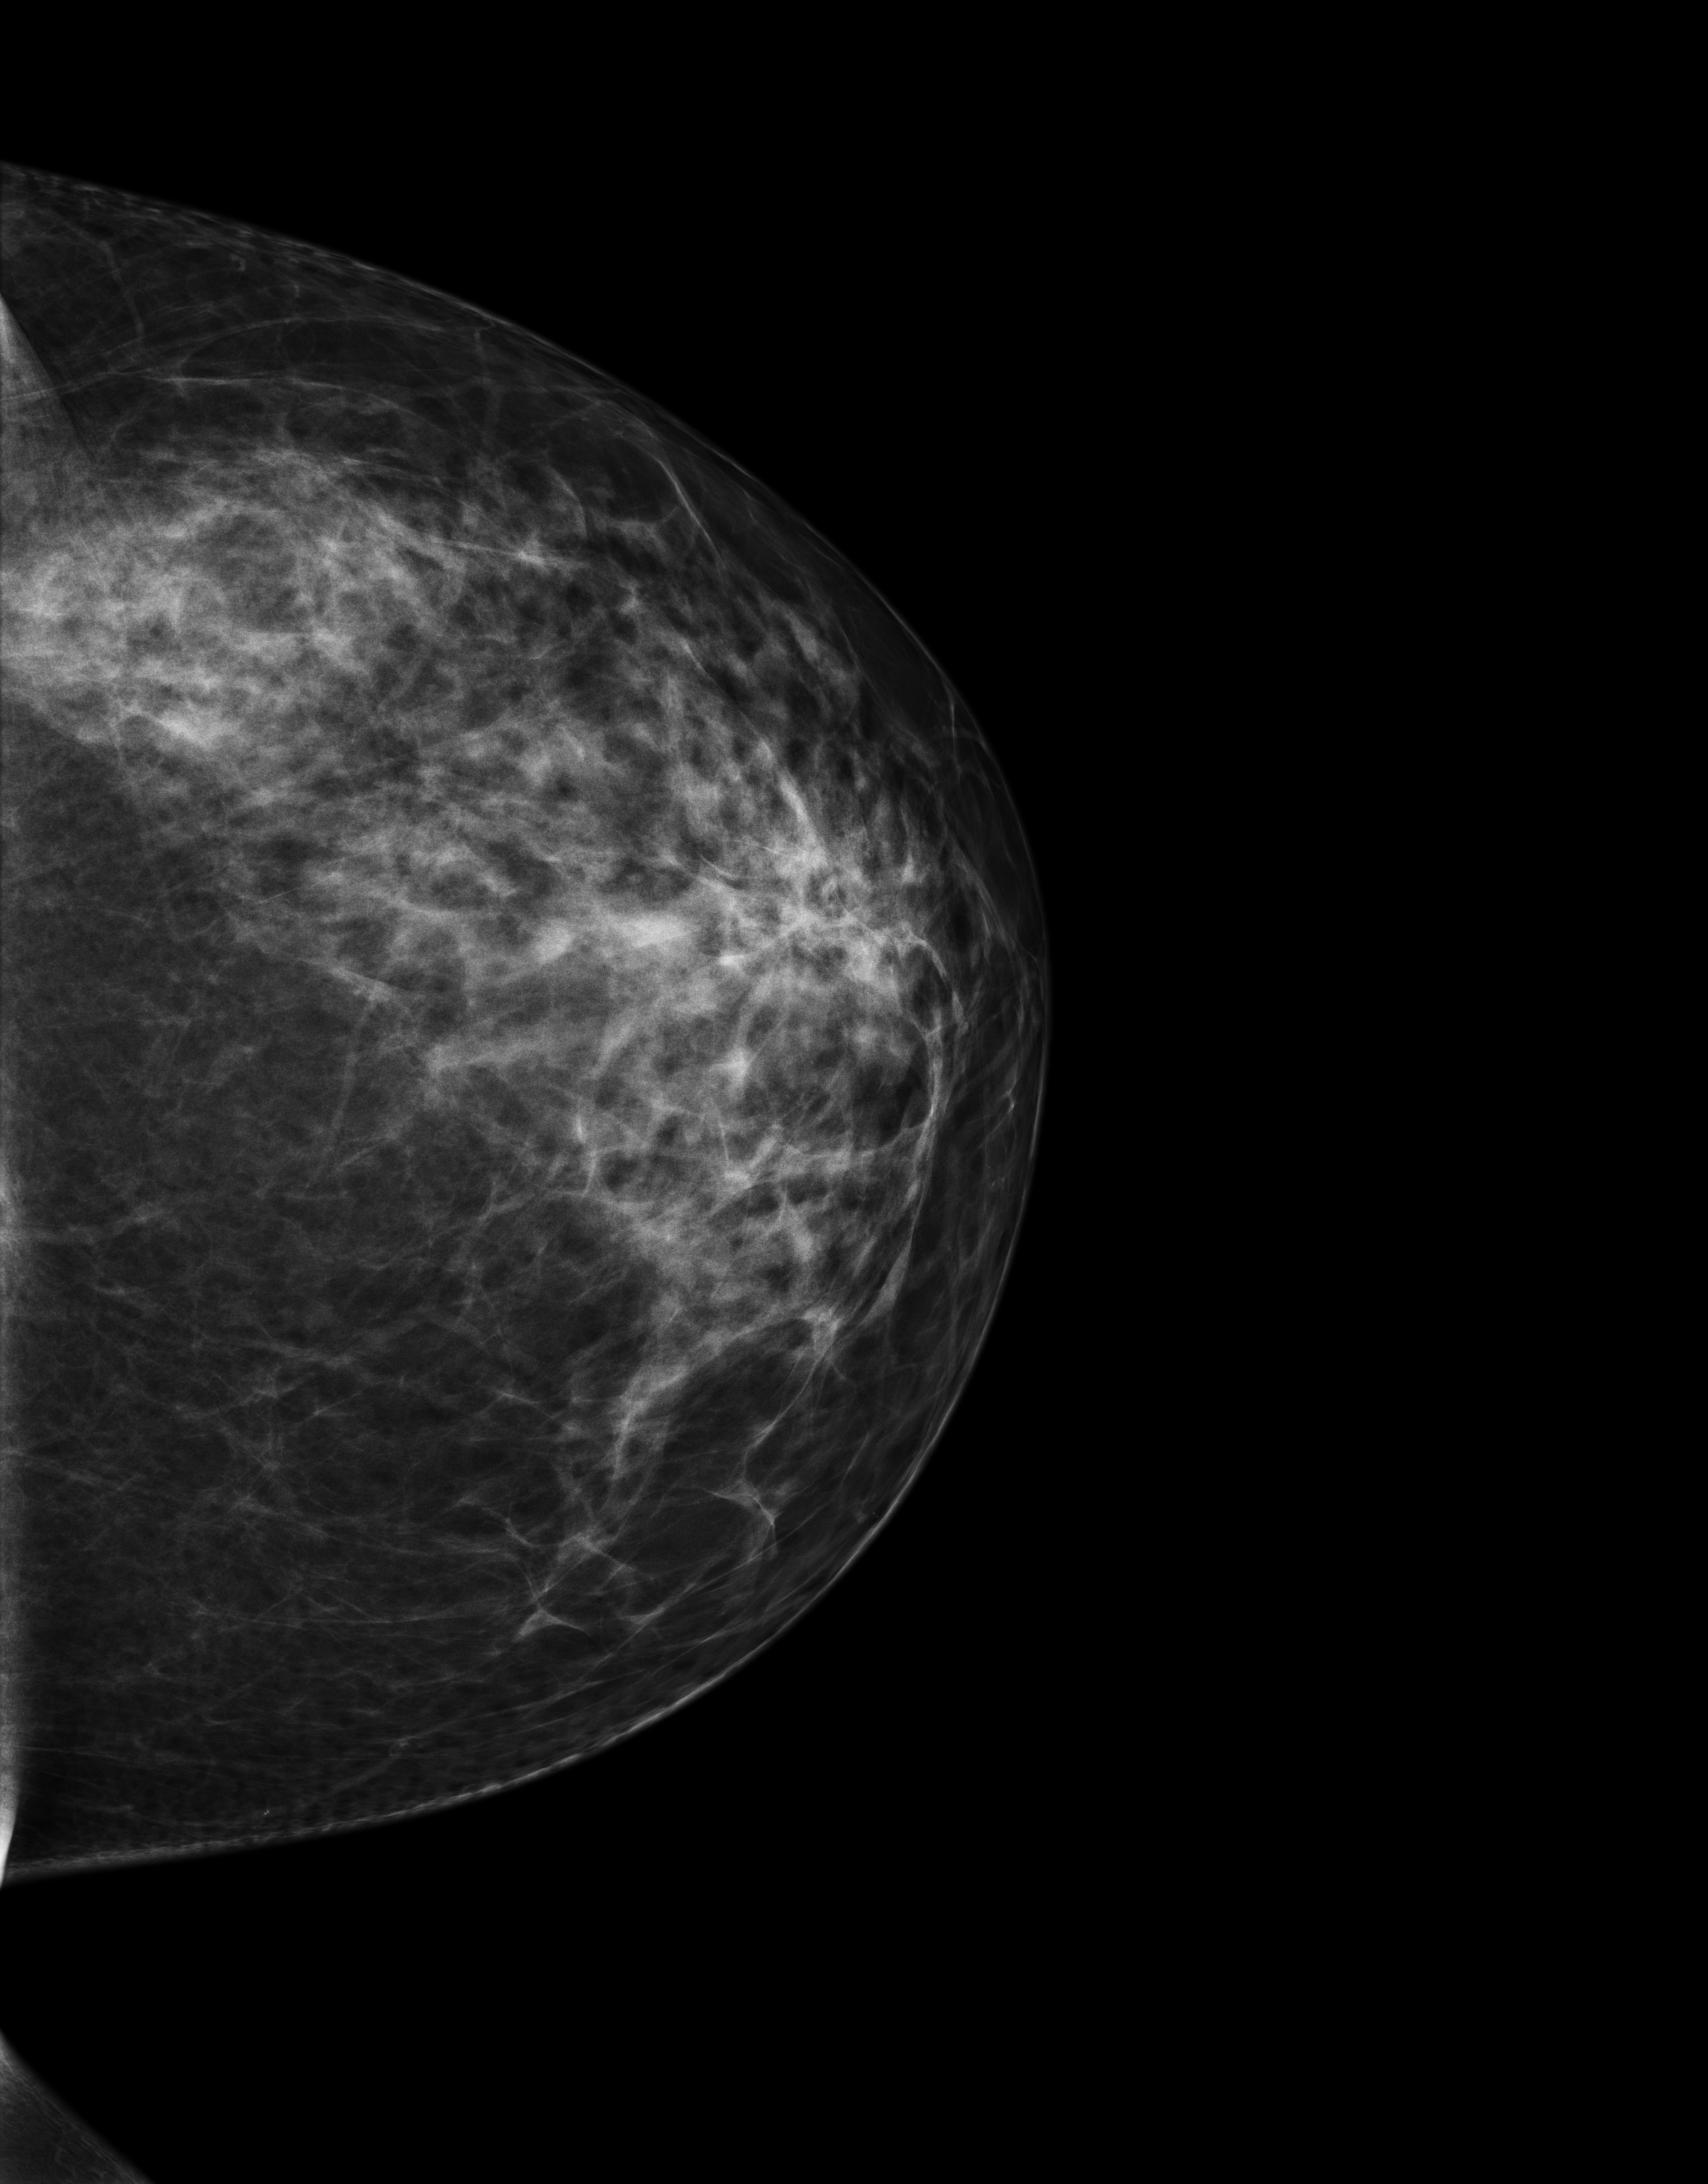
Full-field digital mammogram (FFDM), left breast, craniocaudal (CC) view, annual screening mammography examination, compressed breast thickness 81 mm. Female patient, age 42 years.
- BI-RADS breast density category at the screening exam (both breasts, scale 1–4): 3
- final BI-RADS category for the screening round (tomosynthesis exam, both breasts): category 1
- recall: no recall after this screen